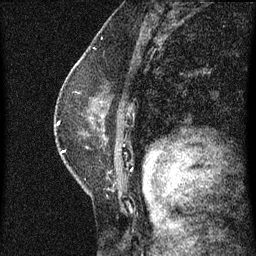
Breast MRI (dynamic contrast-enhanced), one sagittal slice. Slice 42 of 60 in the series (ordered by position). Dynamic contrast-enhanced series, image 2 of 3 at this slice position (ordered by acquisition). 1.5 T. TE 4.2 ms, TR 8 ms. 2 mm slice thickness. 256 × 256 image matrix, field of view 180 × 180 mm. Patient: female, 47 years.
Outlined on this slice (semi-automatically segmented with operator editing):
- analysis volume of interest (the breast-tissue region the enhancement analysis was run in; not a lesion): box from (x=55, y=80) to (x=133, y=187) px
- tumour enhancement mask (voxels above the 70 % enhancement threshold inside the analysis volume of interest): (x=58, y=116)–(x=104, y=153)